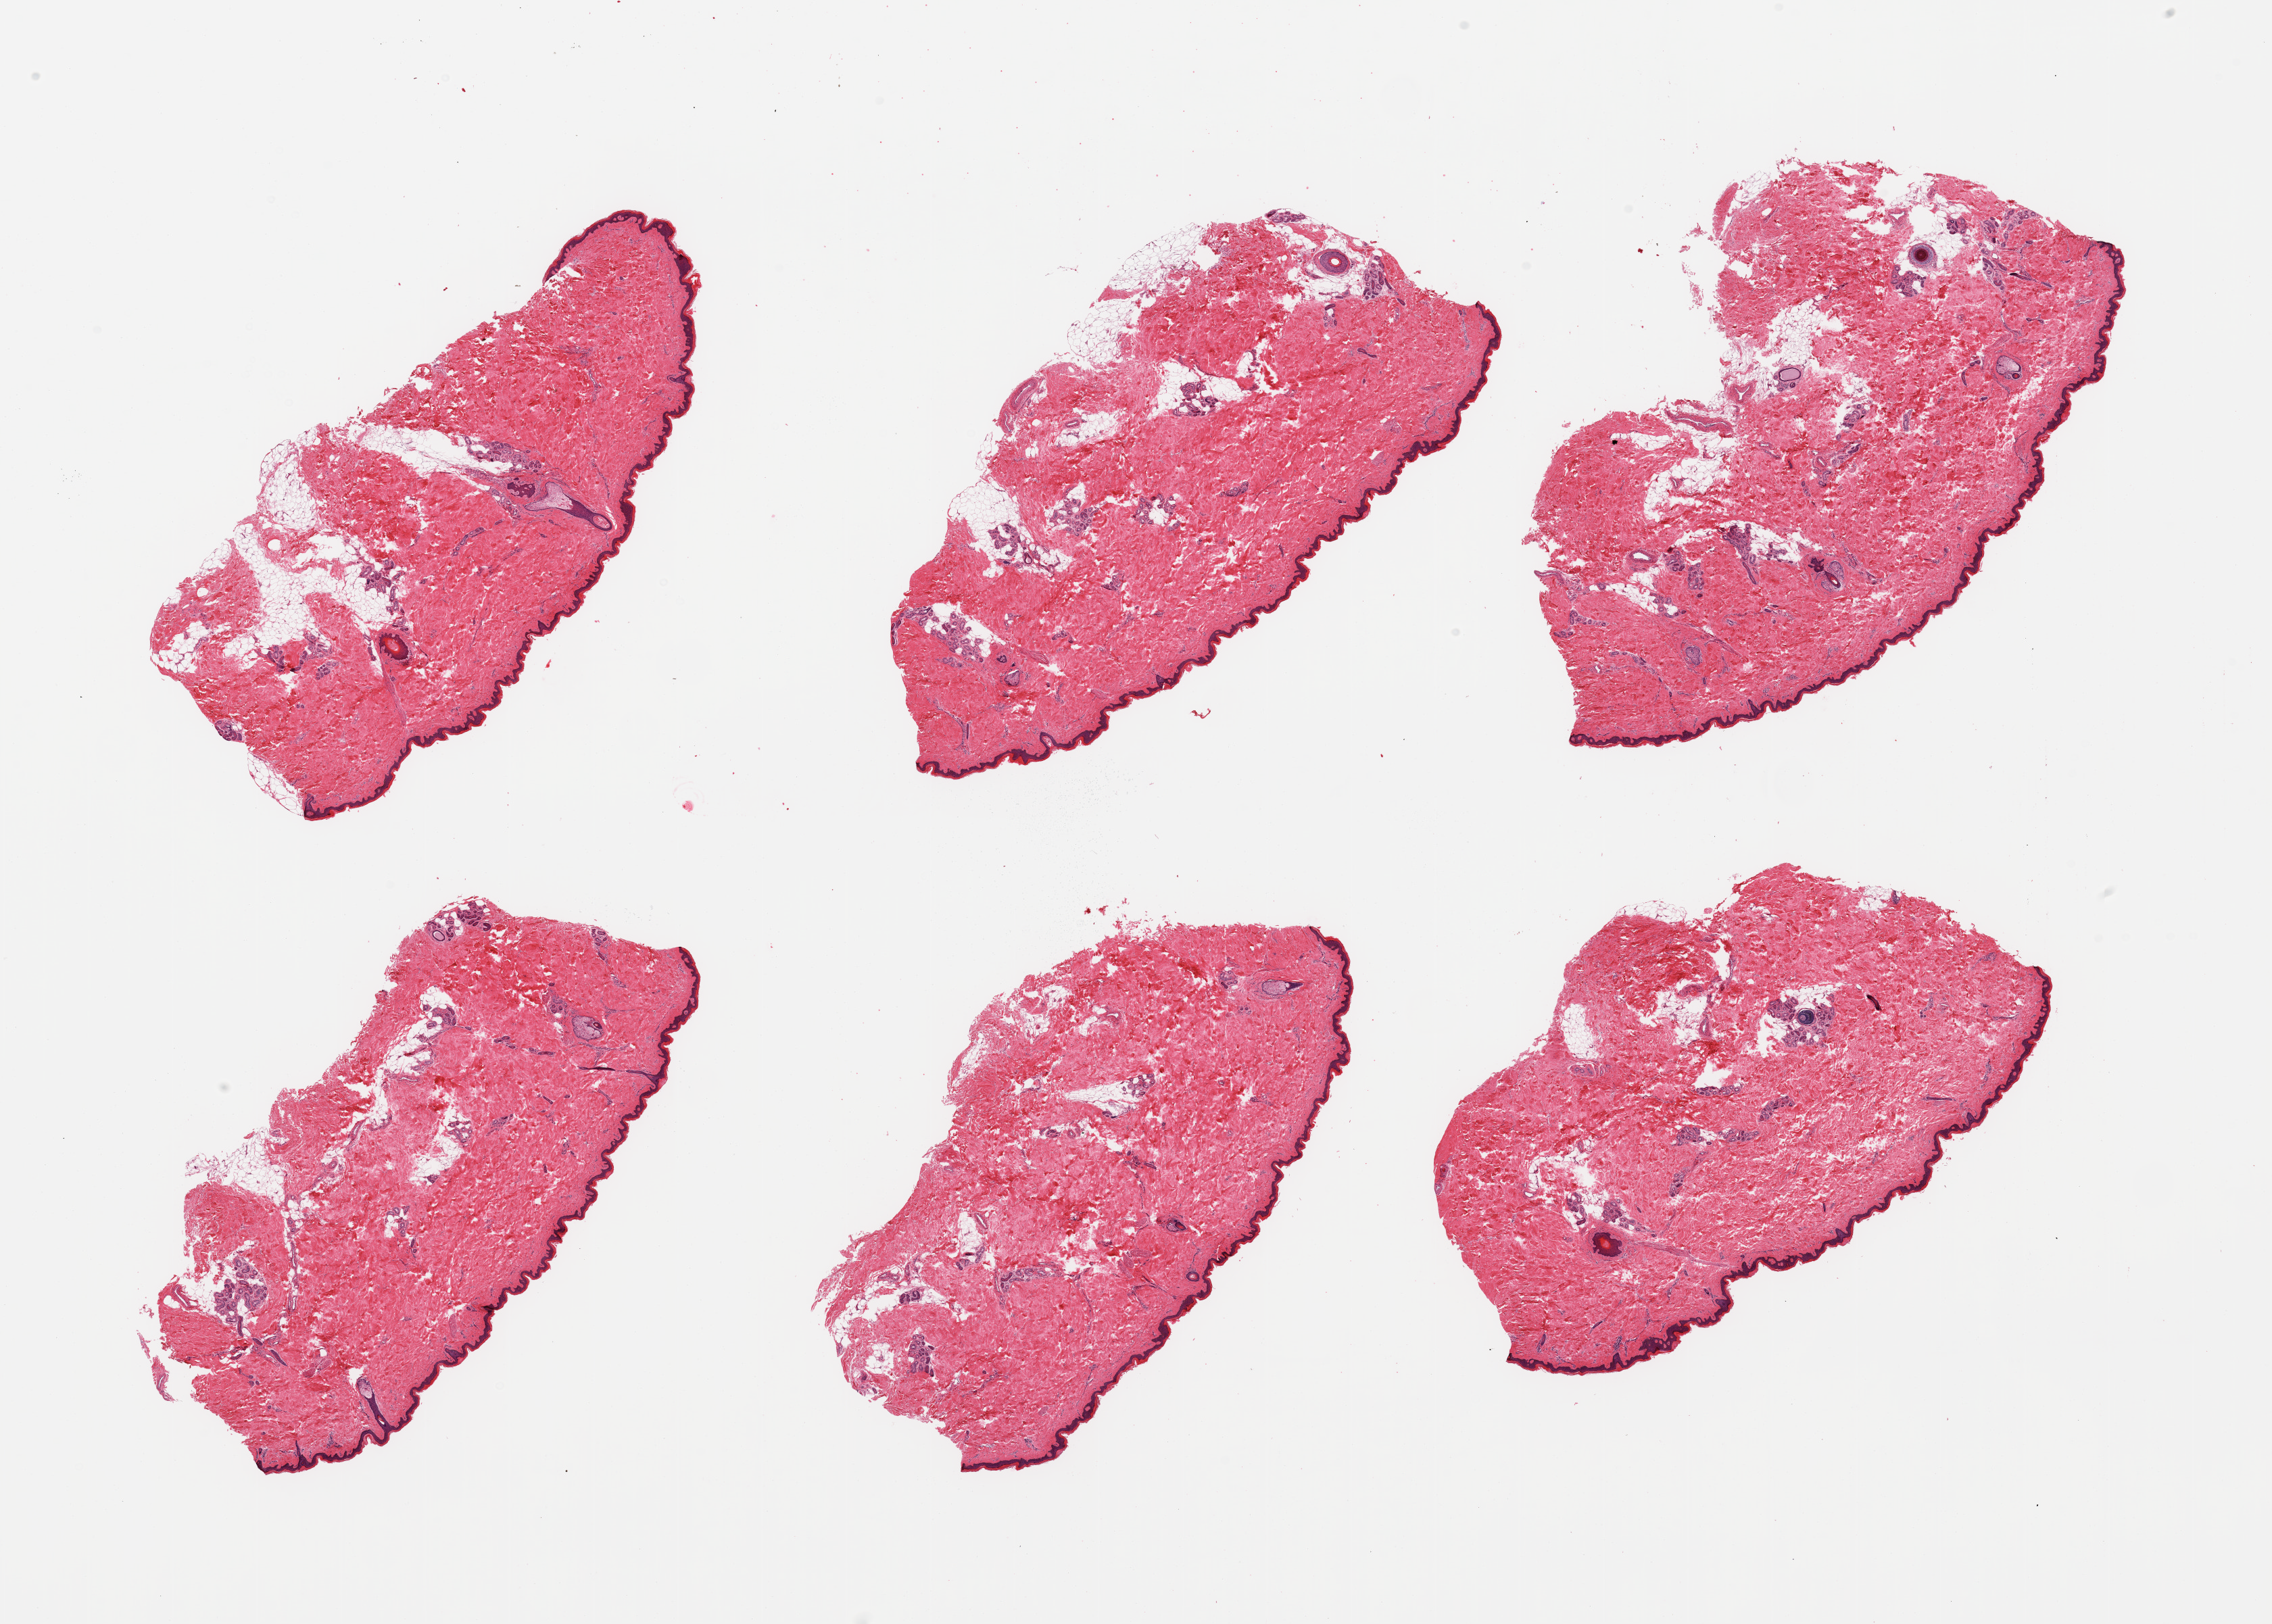
Whole-slide image, haematoxylin and eosin stain, brightfield, low-resolution overview of the scanned area, about 26.6 x 19.0 mm (slide scanned at 20x); PAXgene-fixed, paraffin-embedded tissue; sampled site (target tissue): skin of lower leg; donor tissue sample.
Review note (as recorded): 6 pieces; include up to ~10% mostly internal fat, epidermis measures 34 microns.